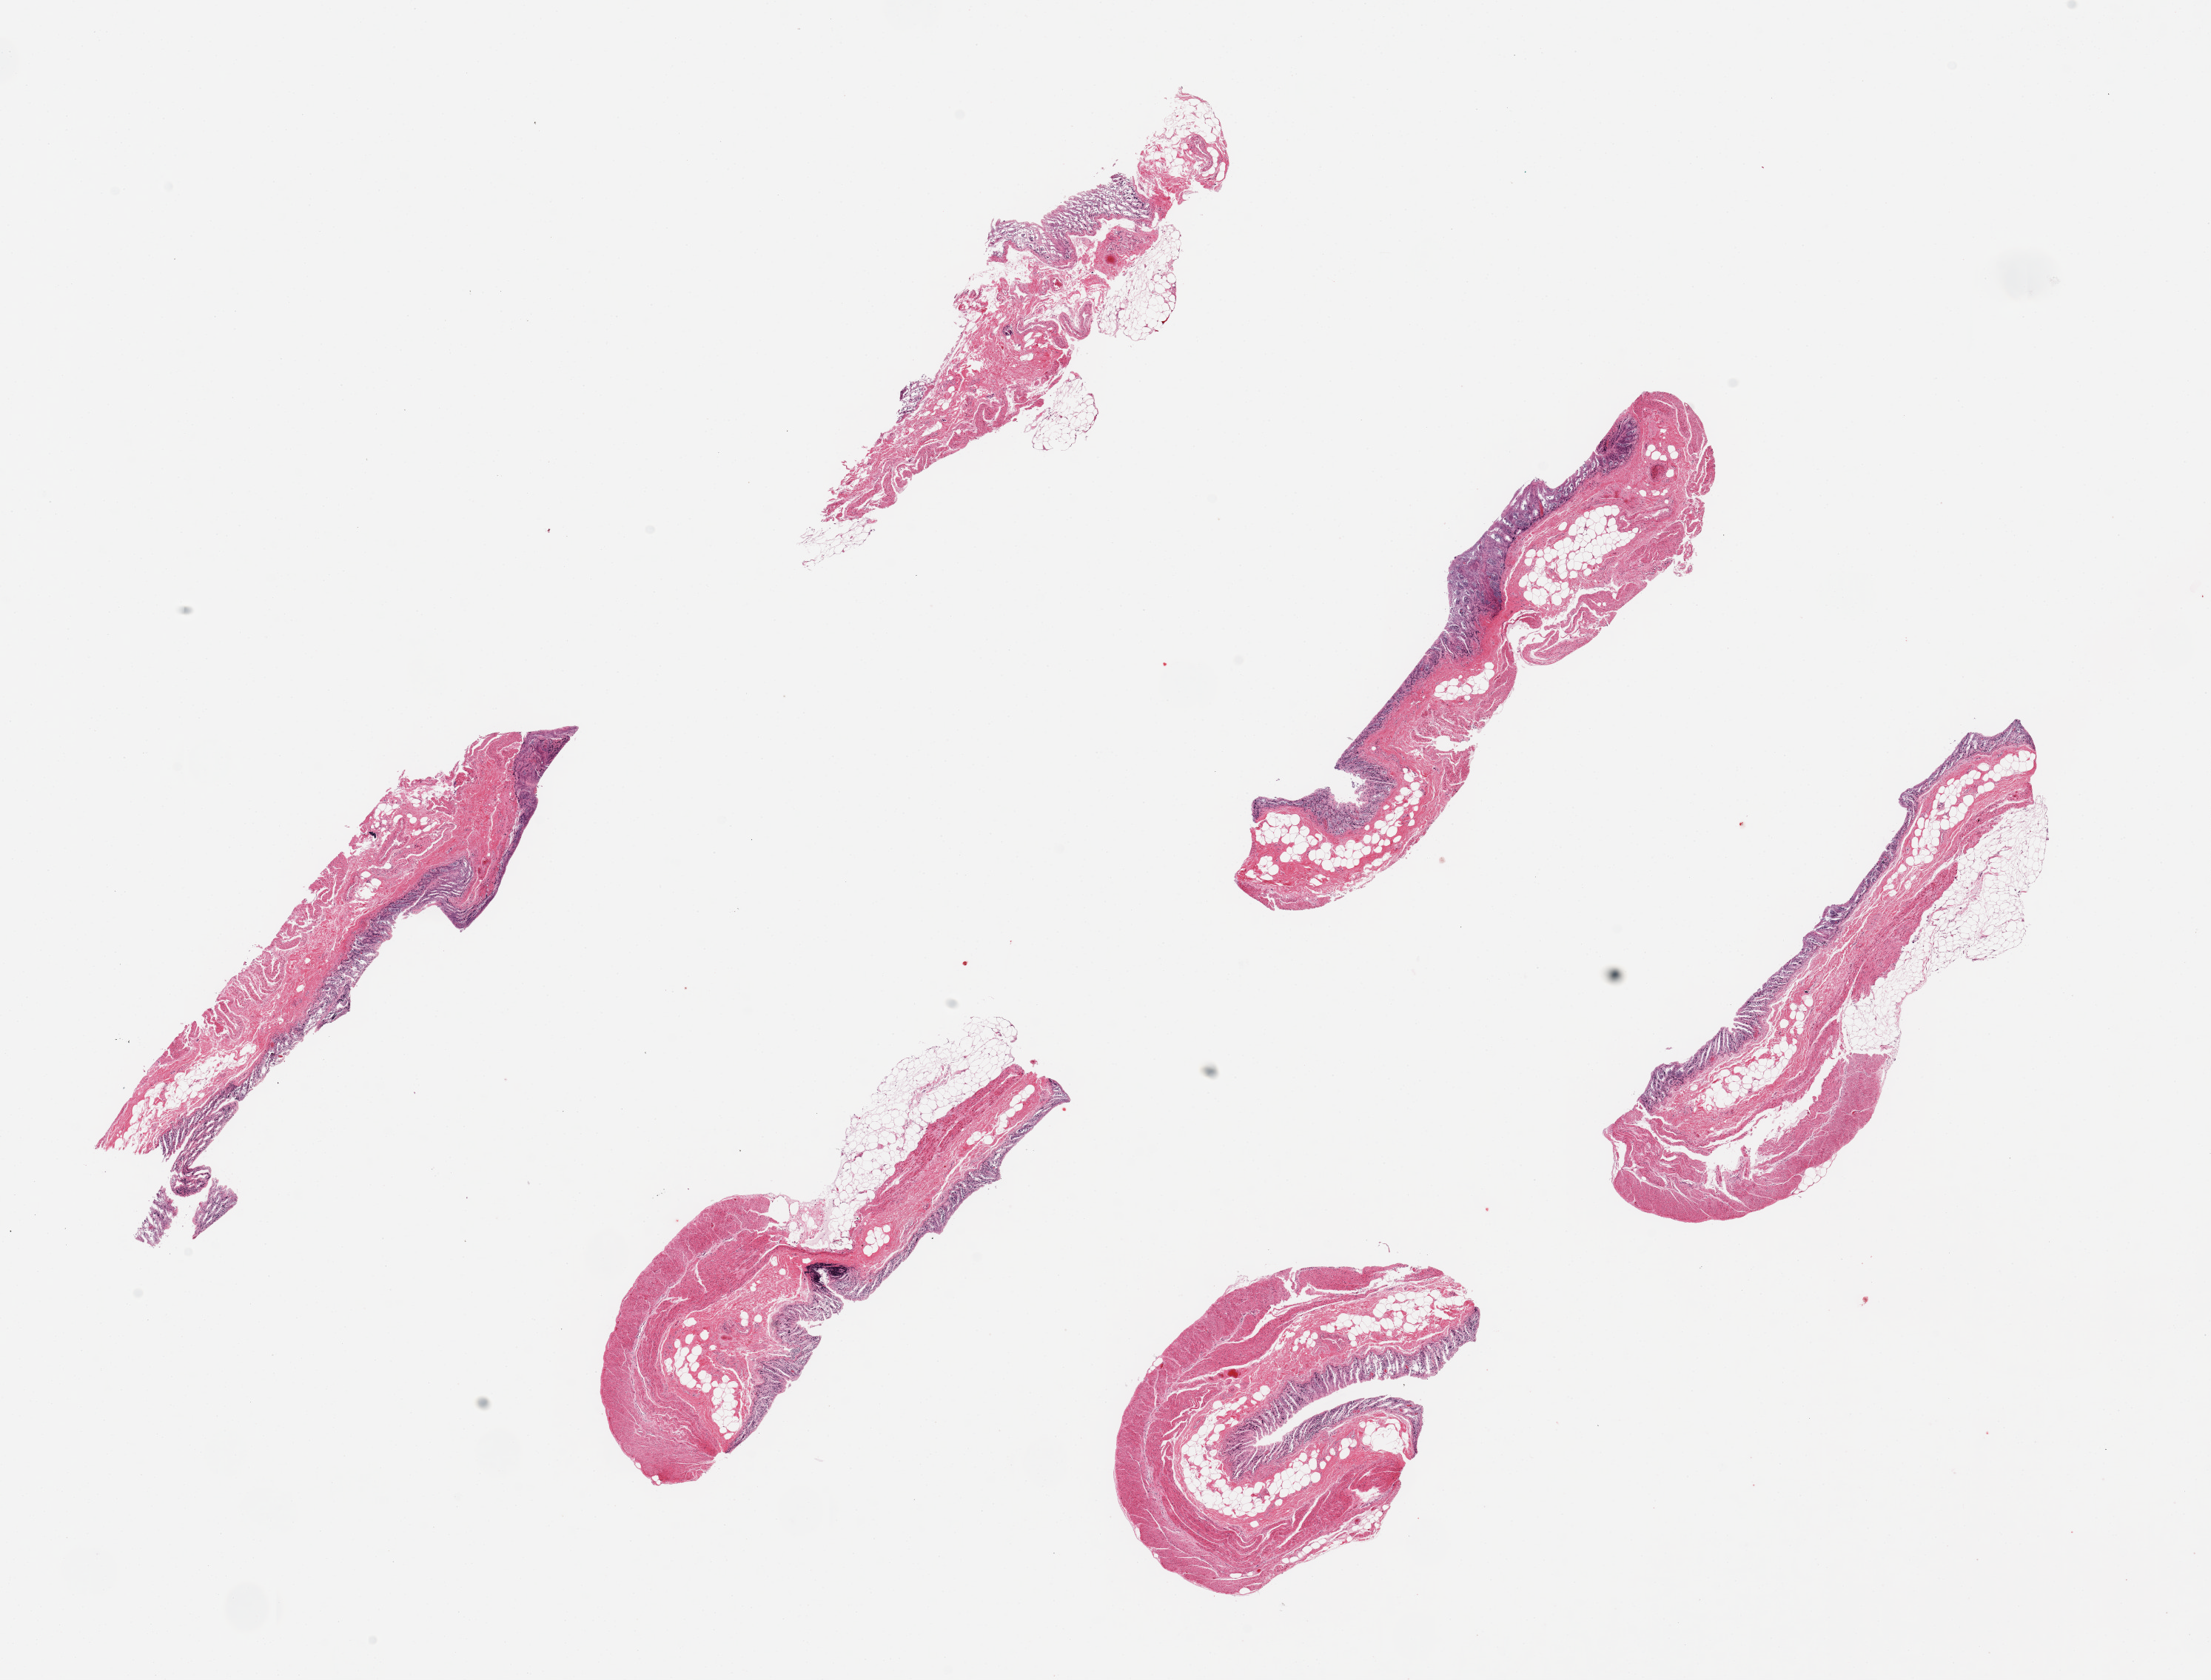
H&E whole-slide image — whole scanned area (about 23.6 x 18.0 mm) shown as a low-resolution overview. PAXgene-fixed, paraffin-embedded tissue. Section of transverse colon (target tissue). Tissue donor sample. Donor: male.
Review note (as recorded): 6 pieces, ~7x1.5mm. Mucosa totally sloughed.